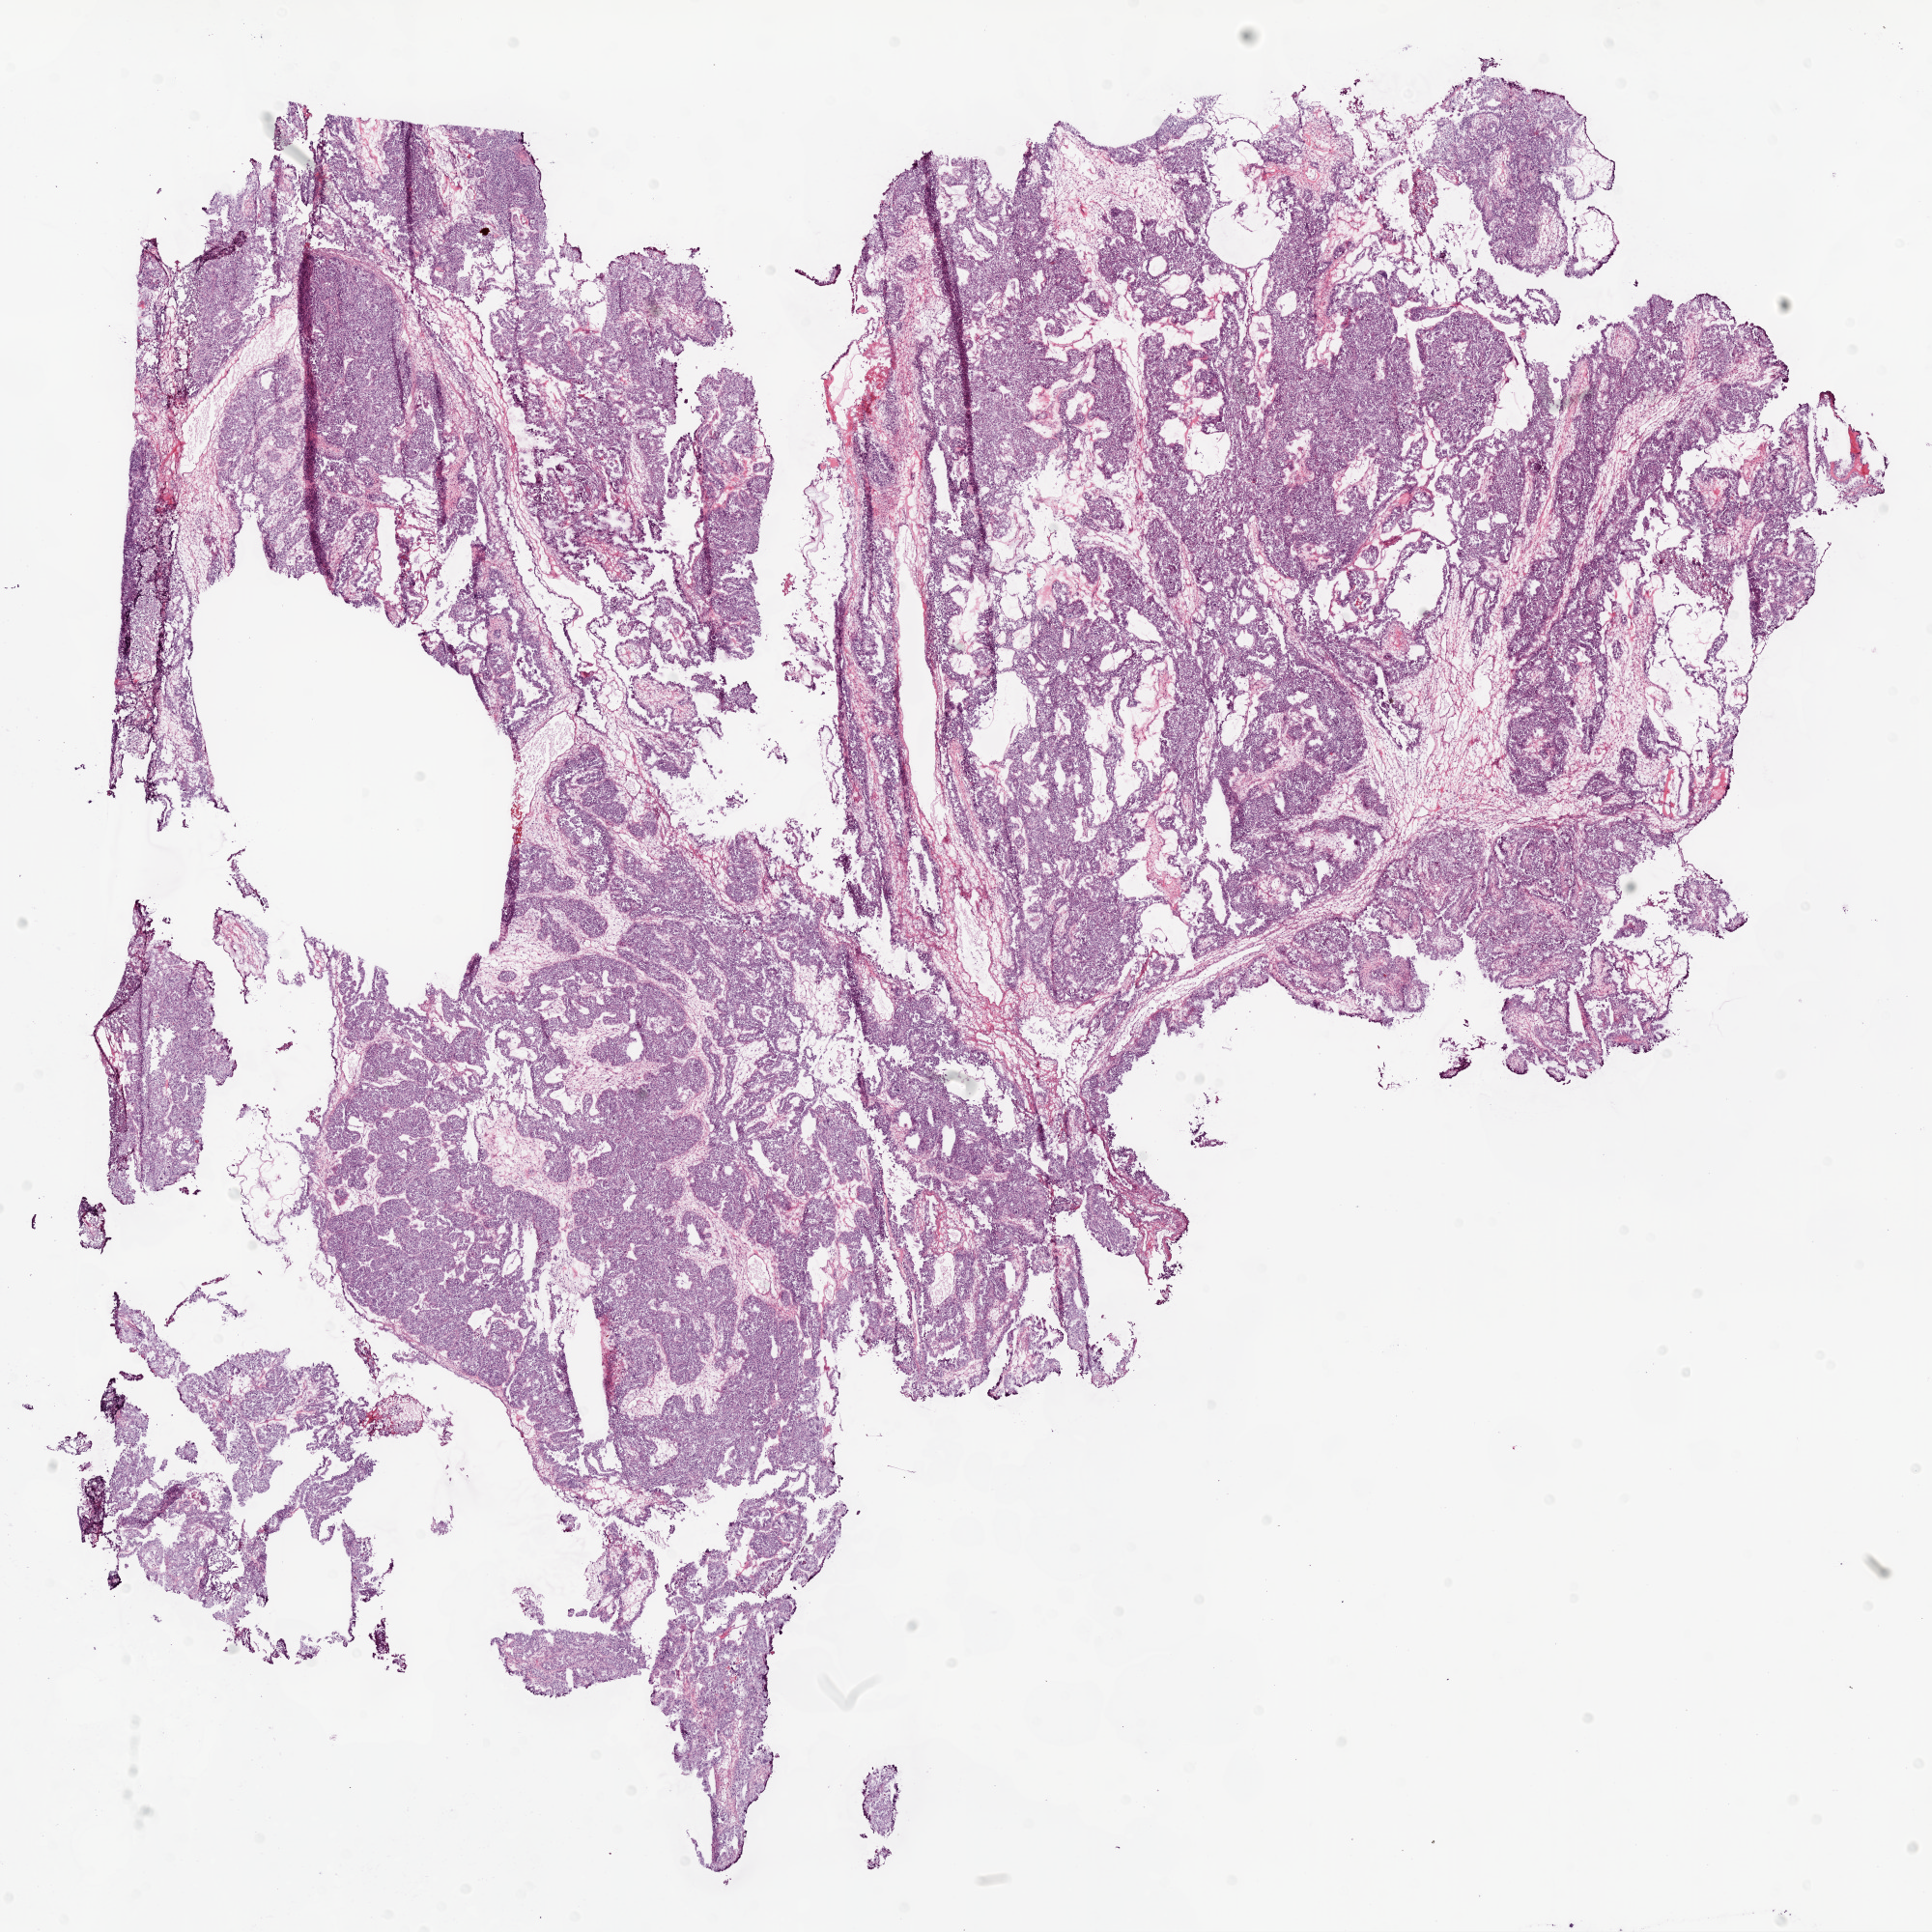
Whole-slide histology image, H&E-stained, whole scanned area (about 16.0 x 16.0 mm, acquisition: 20x scan) shown as a low-resolution overview; frozen section; primary tumour sample from the ovary. Patient: female, age at initial diagnosis 43 years. Histologic grade: G2 (moderately differentiated). Composition of this section per pathologist review: tumour cells 95%, tumour nuclei 75%, normal cells 0%, stromal cells 0%, necrosis 5%.
Laterality: bilateral. Histologic diagnosis: Serous cystadenocarcinoma, NOS. FIGO stage: IIC.